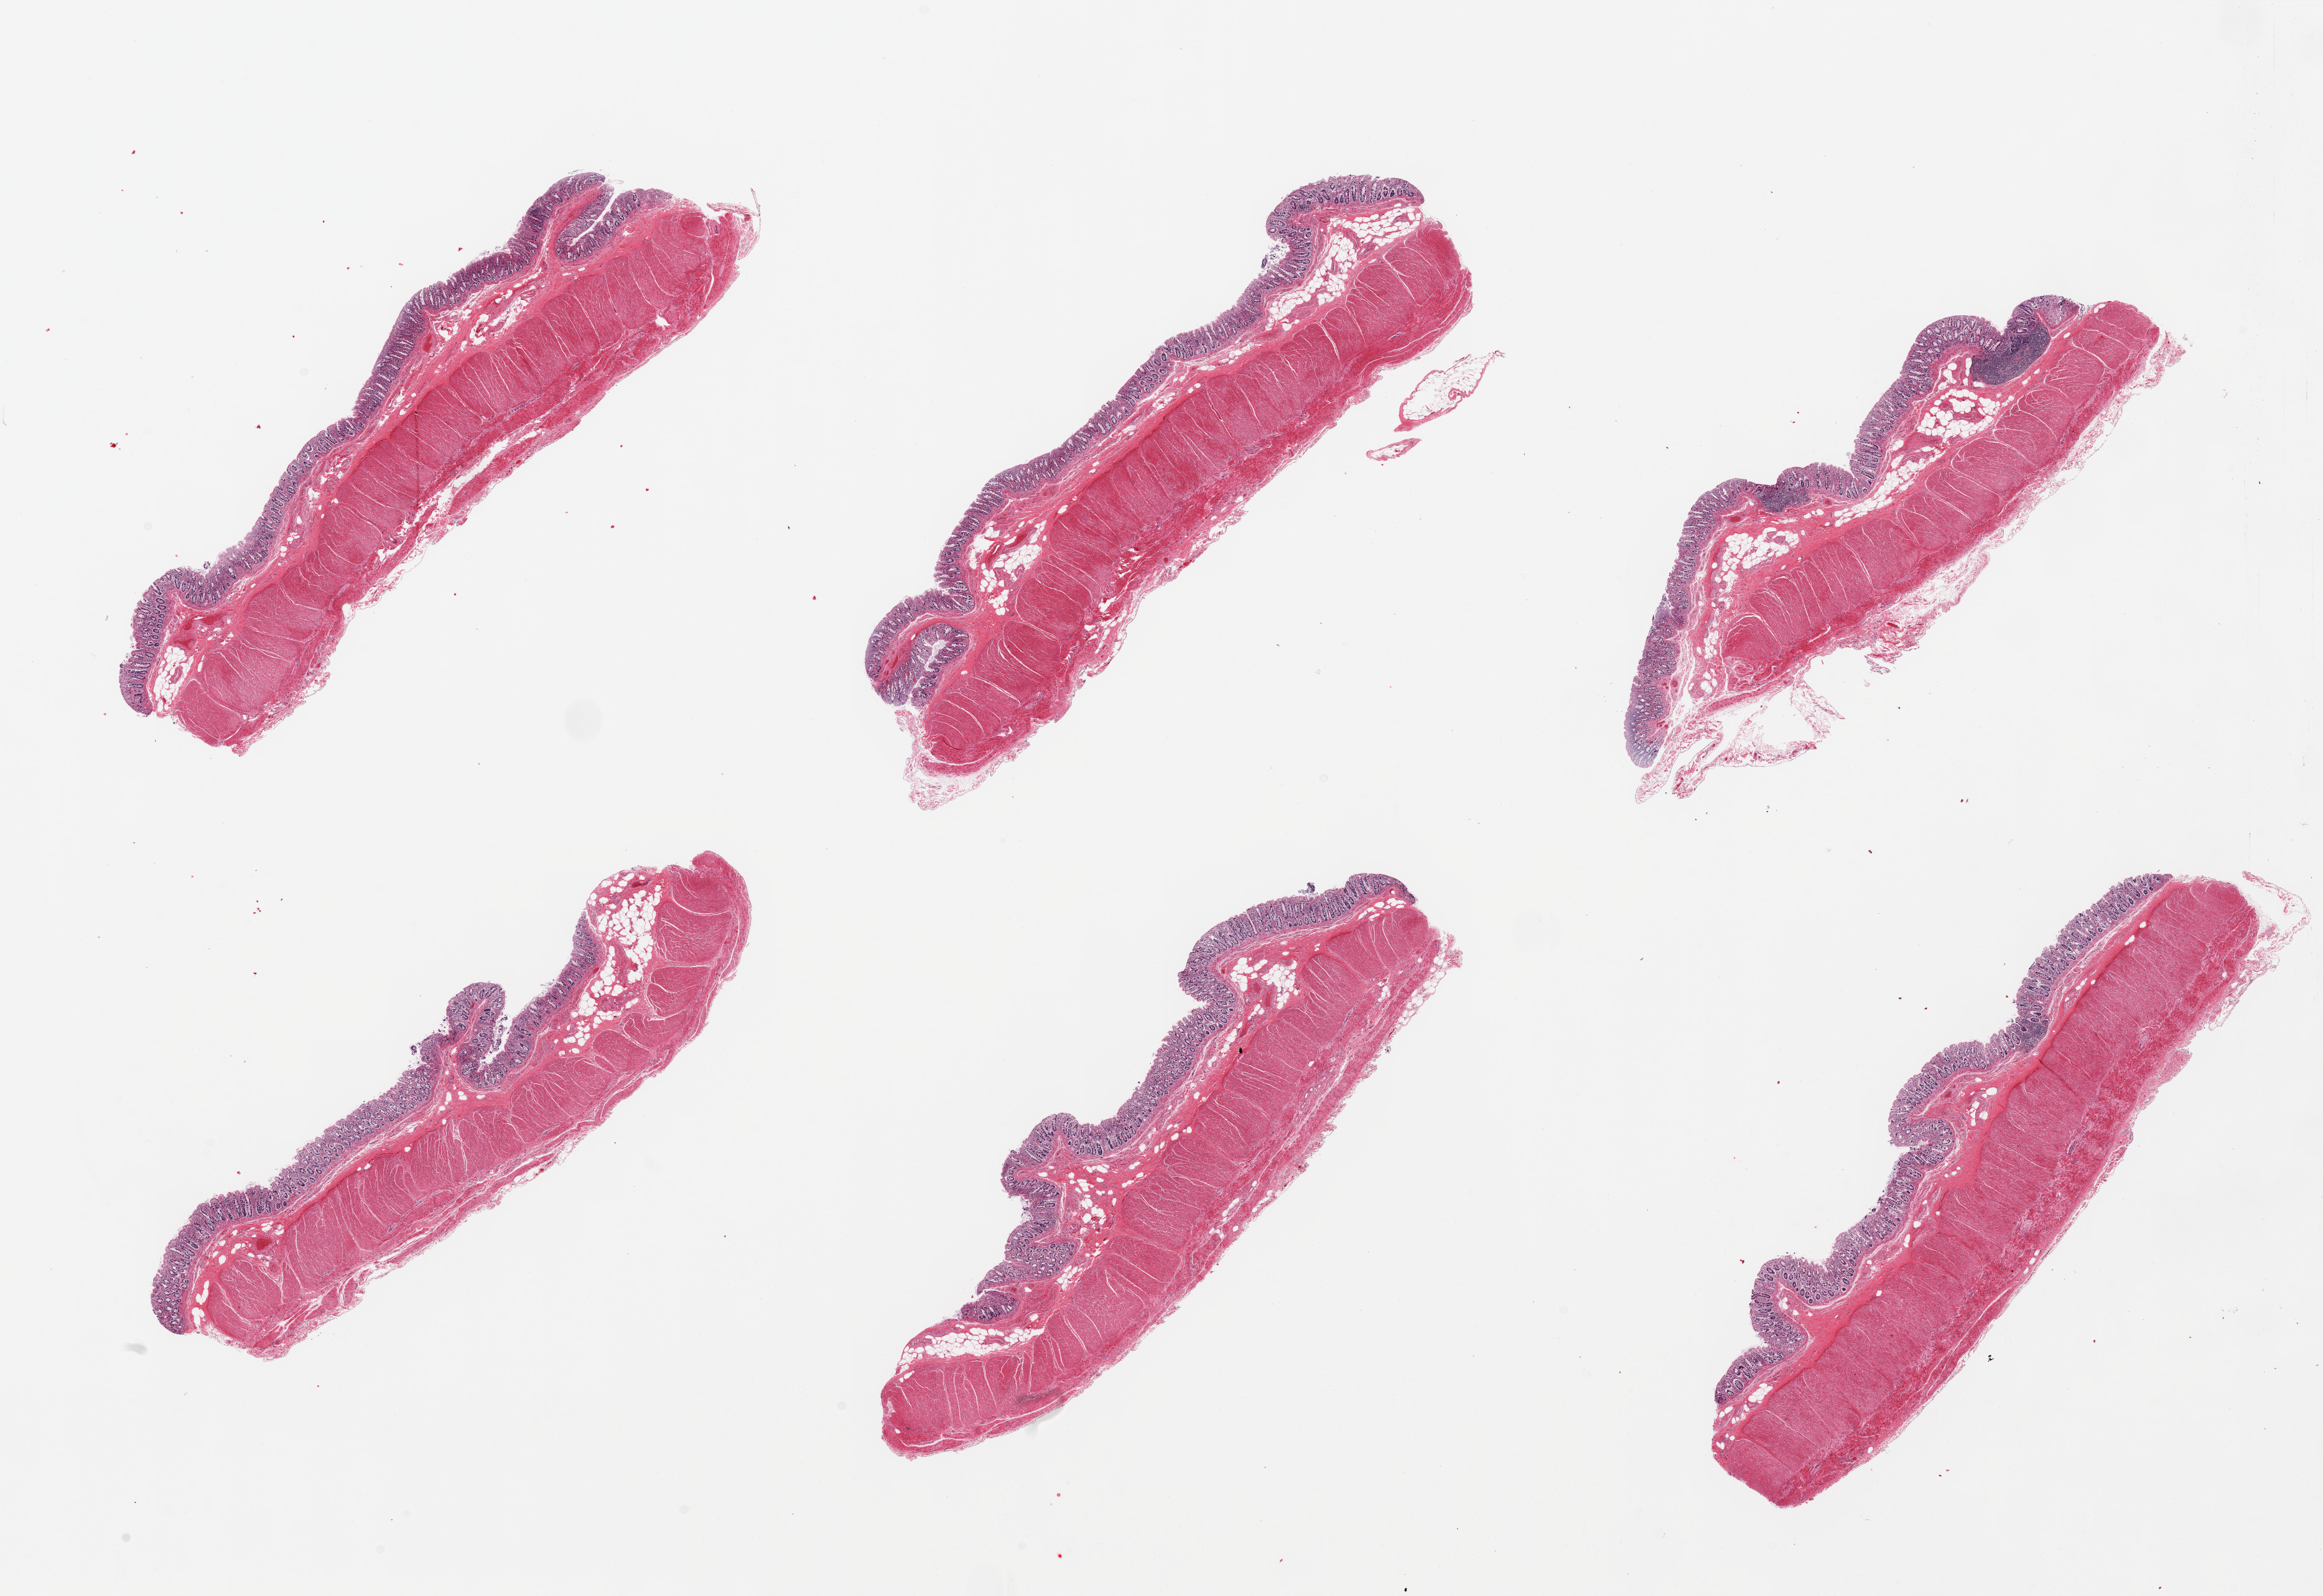
Digitized H&E-stained section, brightfield — low-resolution overview of the scanned area, about 29.5 x 20.3 mm (acquisition: 20x scan); PAXgene-fixed, paraffin-embedded tissue; target tissue: transverse colon; donor tissue sample. Donor: male.
* pathologist's review note for this sample: 6 pieces, mucosa moderately-markedly autolyzed, ~0.3mm, ~10-15% thickness